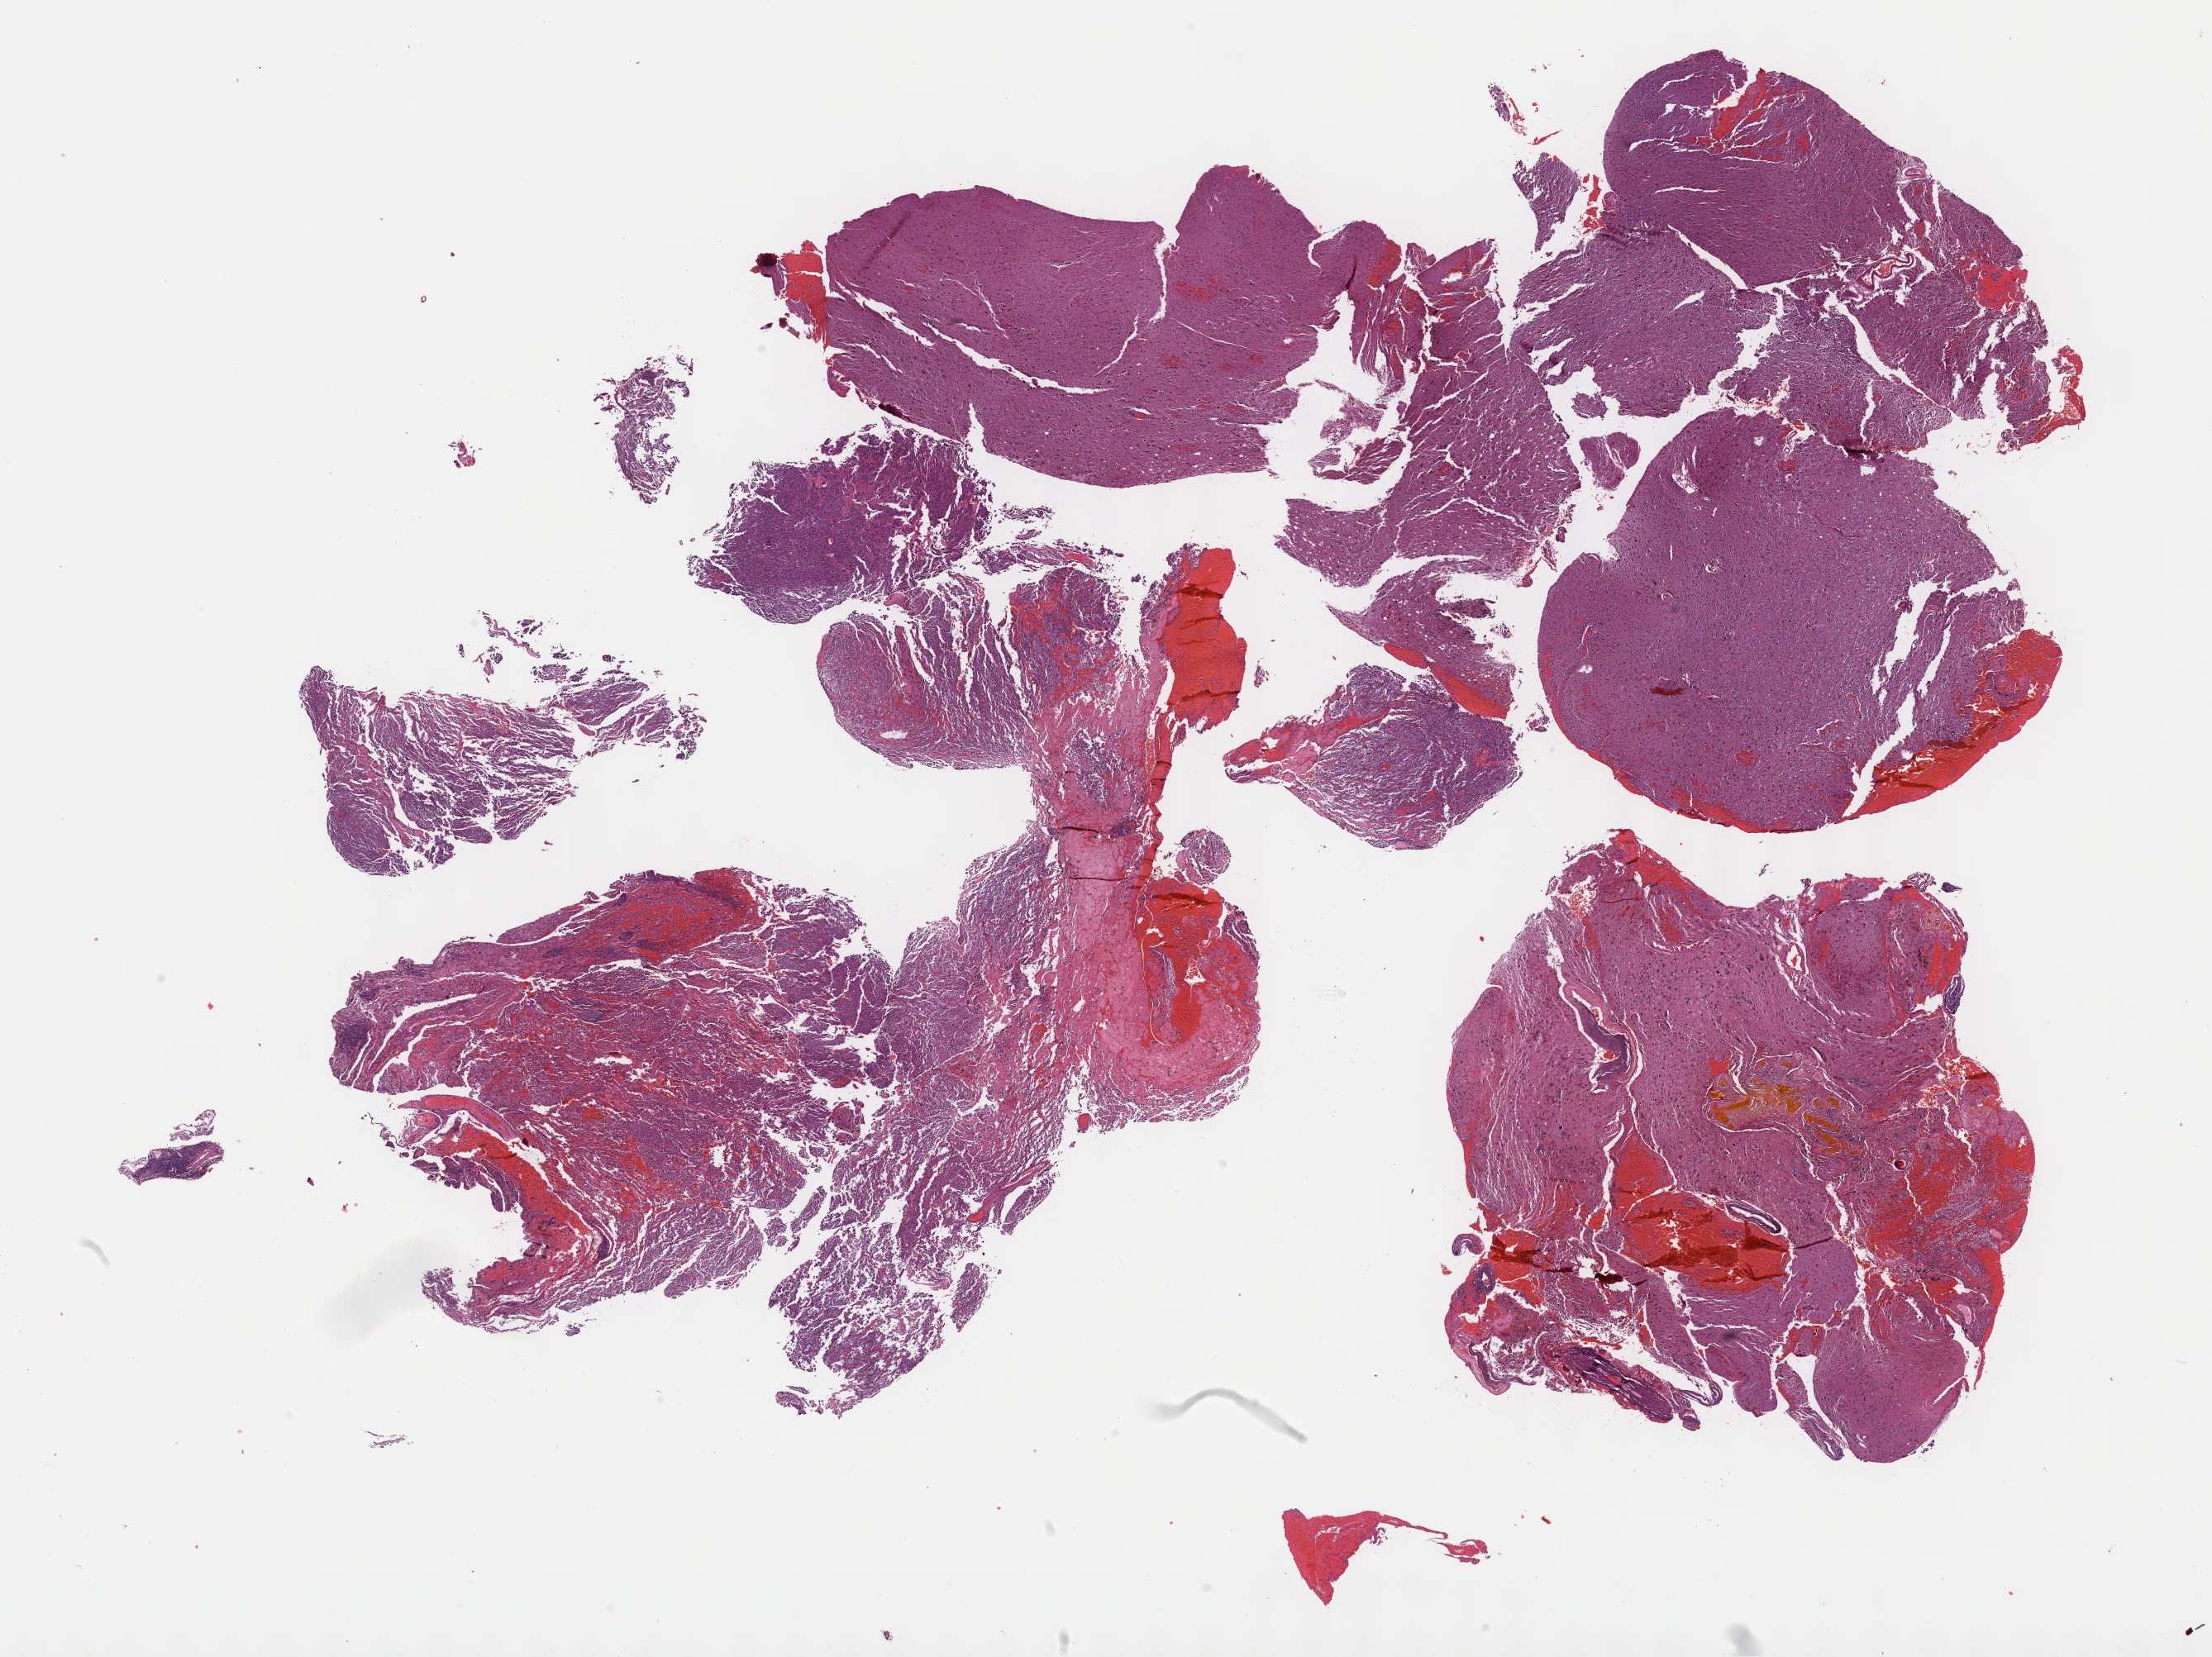
H&E whole-slide image, low-resolution overview of the scanned area, about 21.6 x 16.2 mm (from a 40x scan); formalin-fixed paraffin-embedded (FFPE) diagnostic section; primary tumour sample from the brain. Male, age 75 years at initial diagnosis. Histologic grade: G3 (poorly differentiated).
Histologic diagnosis: Oligodendroglioma, anaplastic.